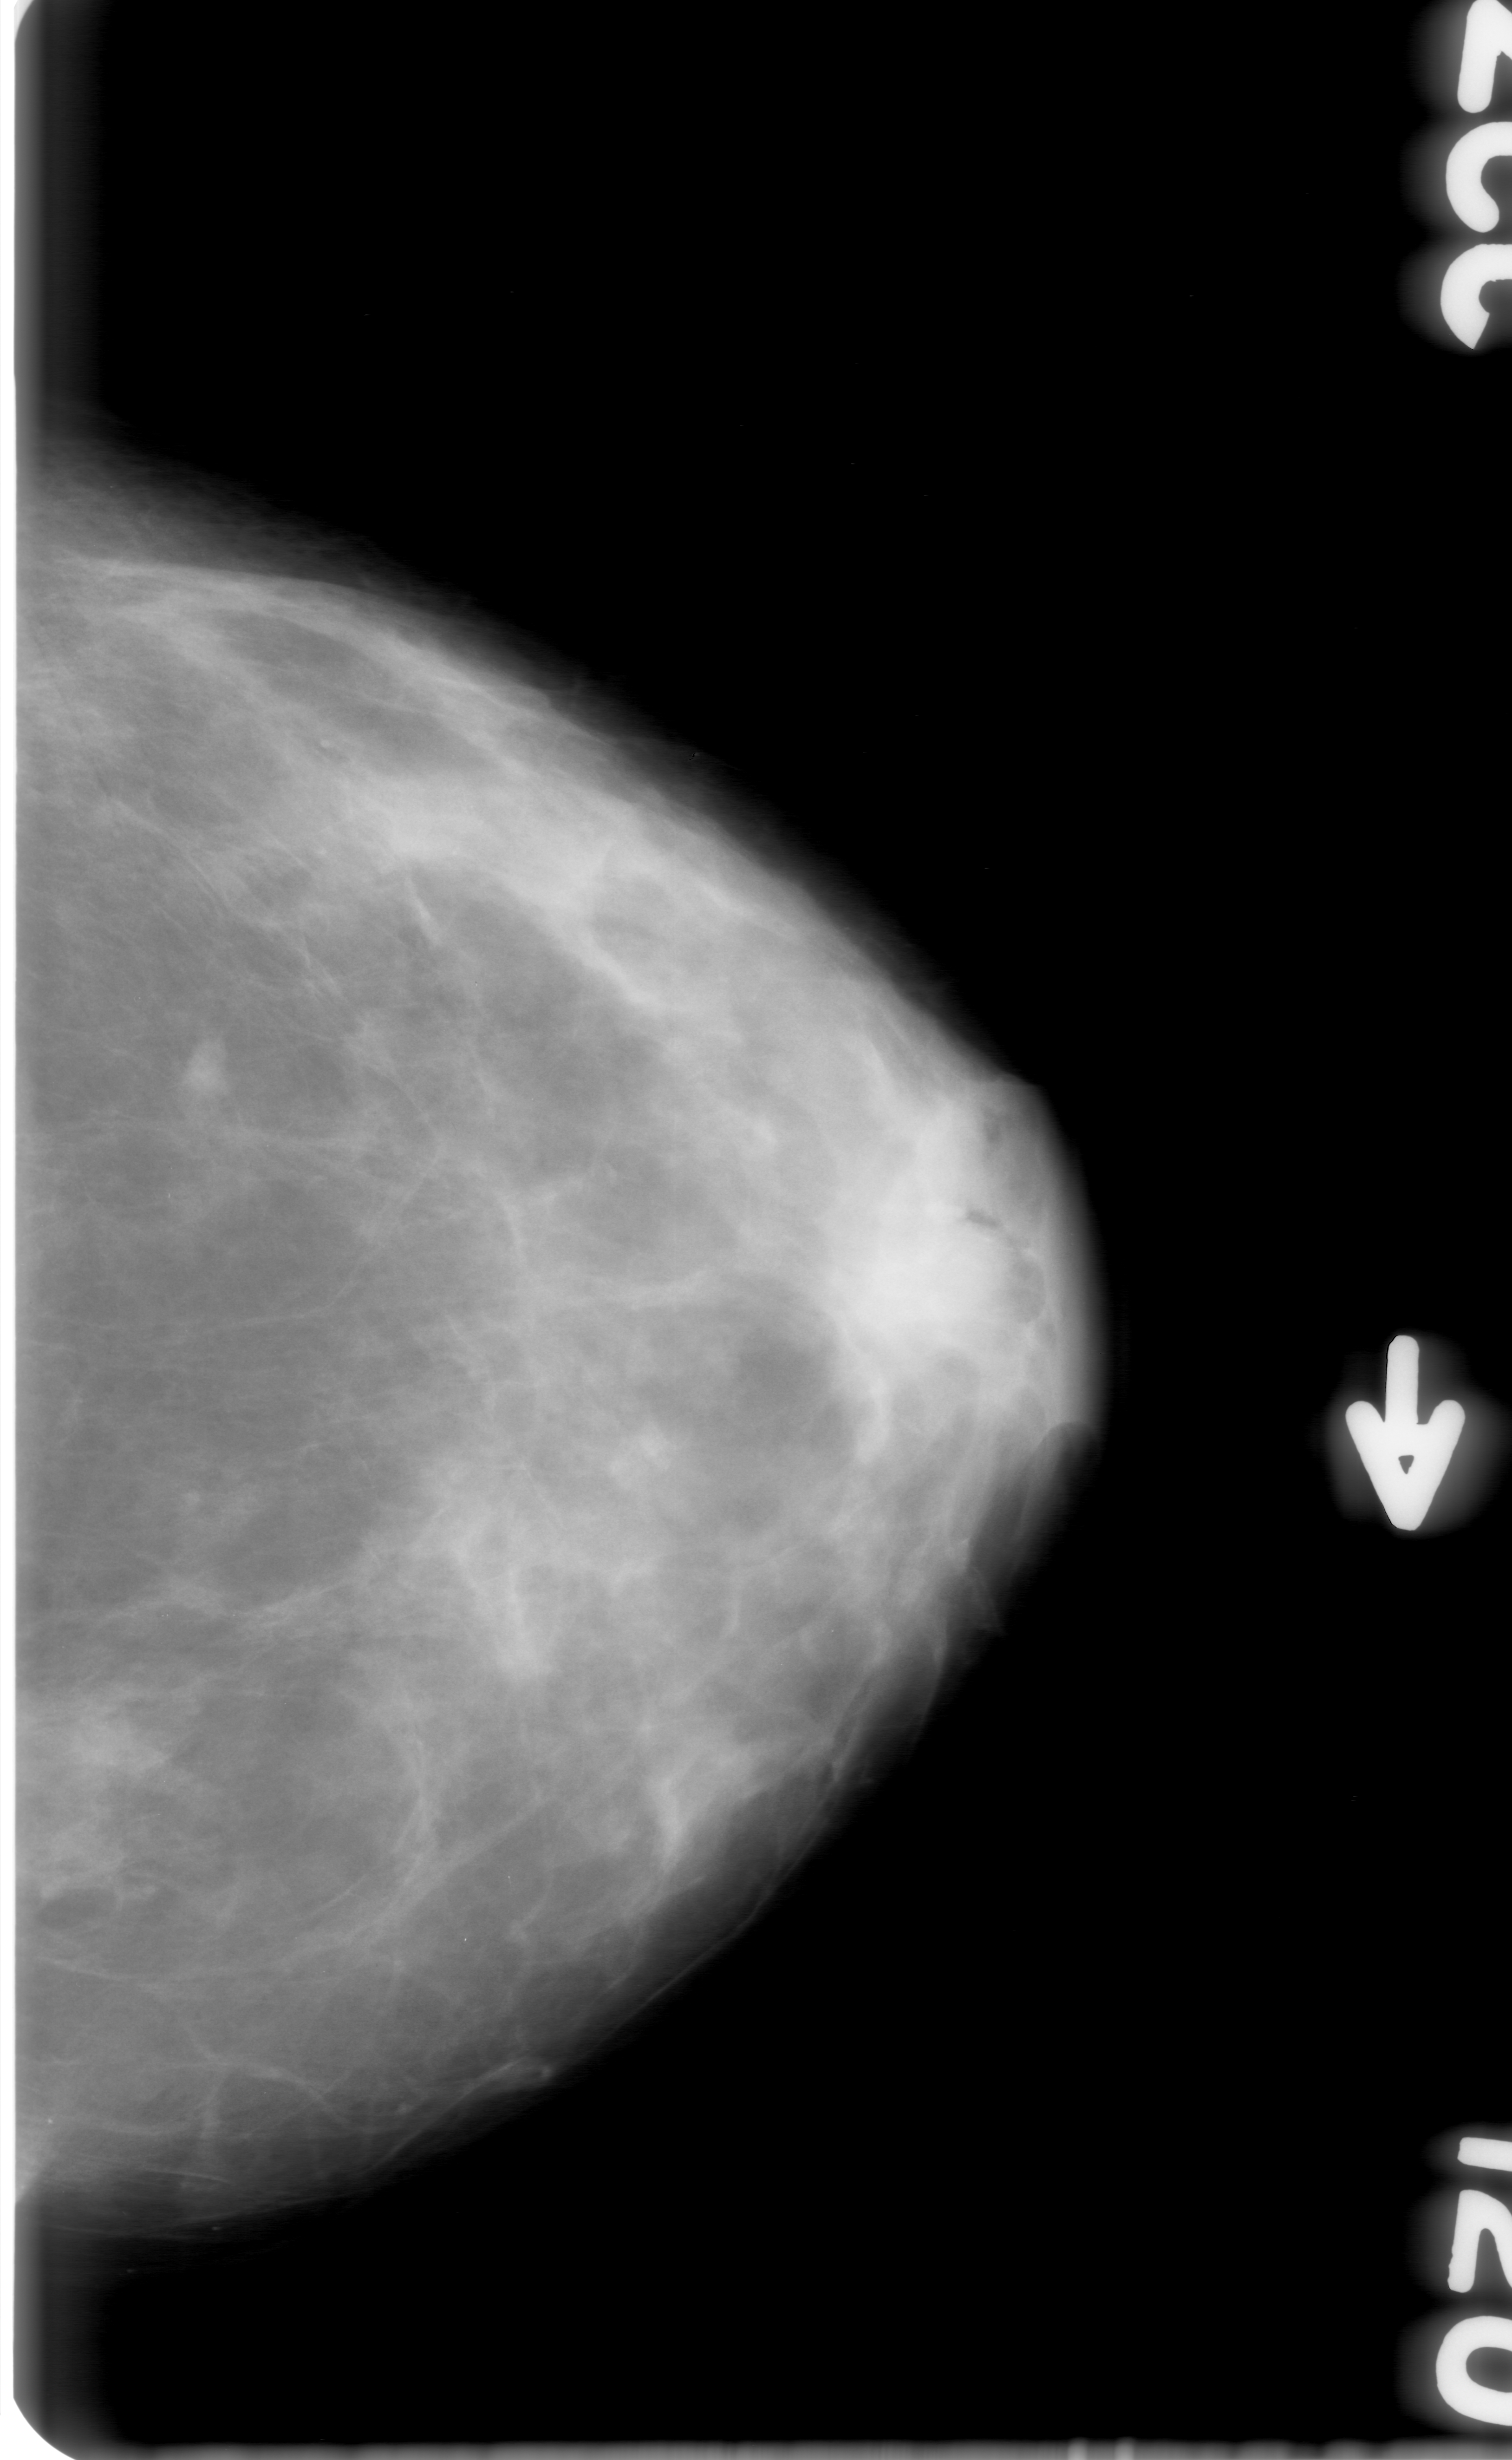
Mammogram (digitized film); left breast; CC view; breast composition: heterogeneously dense (BI-RADS density category 3 of 4); 1512 × 2460 image matrix.
Expert-marked regions of interest on this image (one box per marked abnormality):
- mass, shape irregular, margins obscured; BI-RADS assessment category 0 (incomplete: needs additional imaging); subtlety rating 3 on a 1 (subtle) to 5 (obvious) scale; pathology result (as recorded, not read from the image): benign: bounding box <175,1038,238,1104> (left, top, right, bottom; pixels)